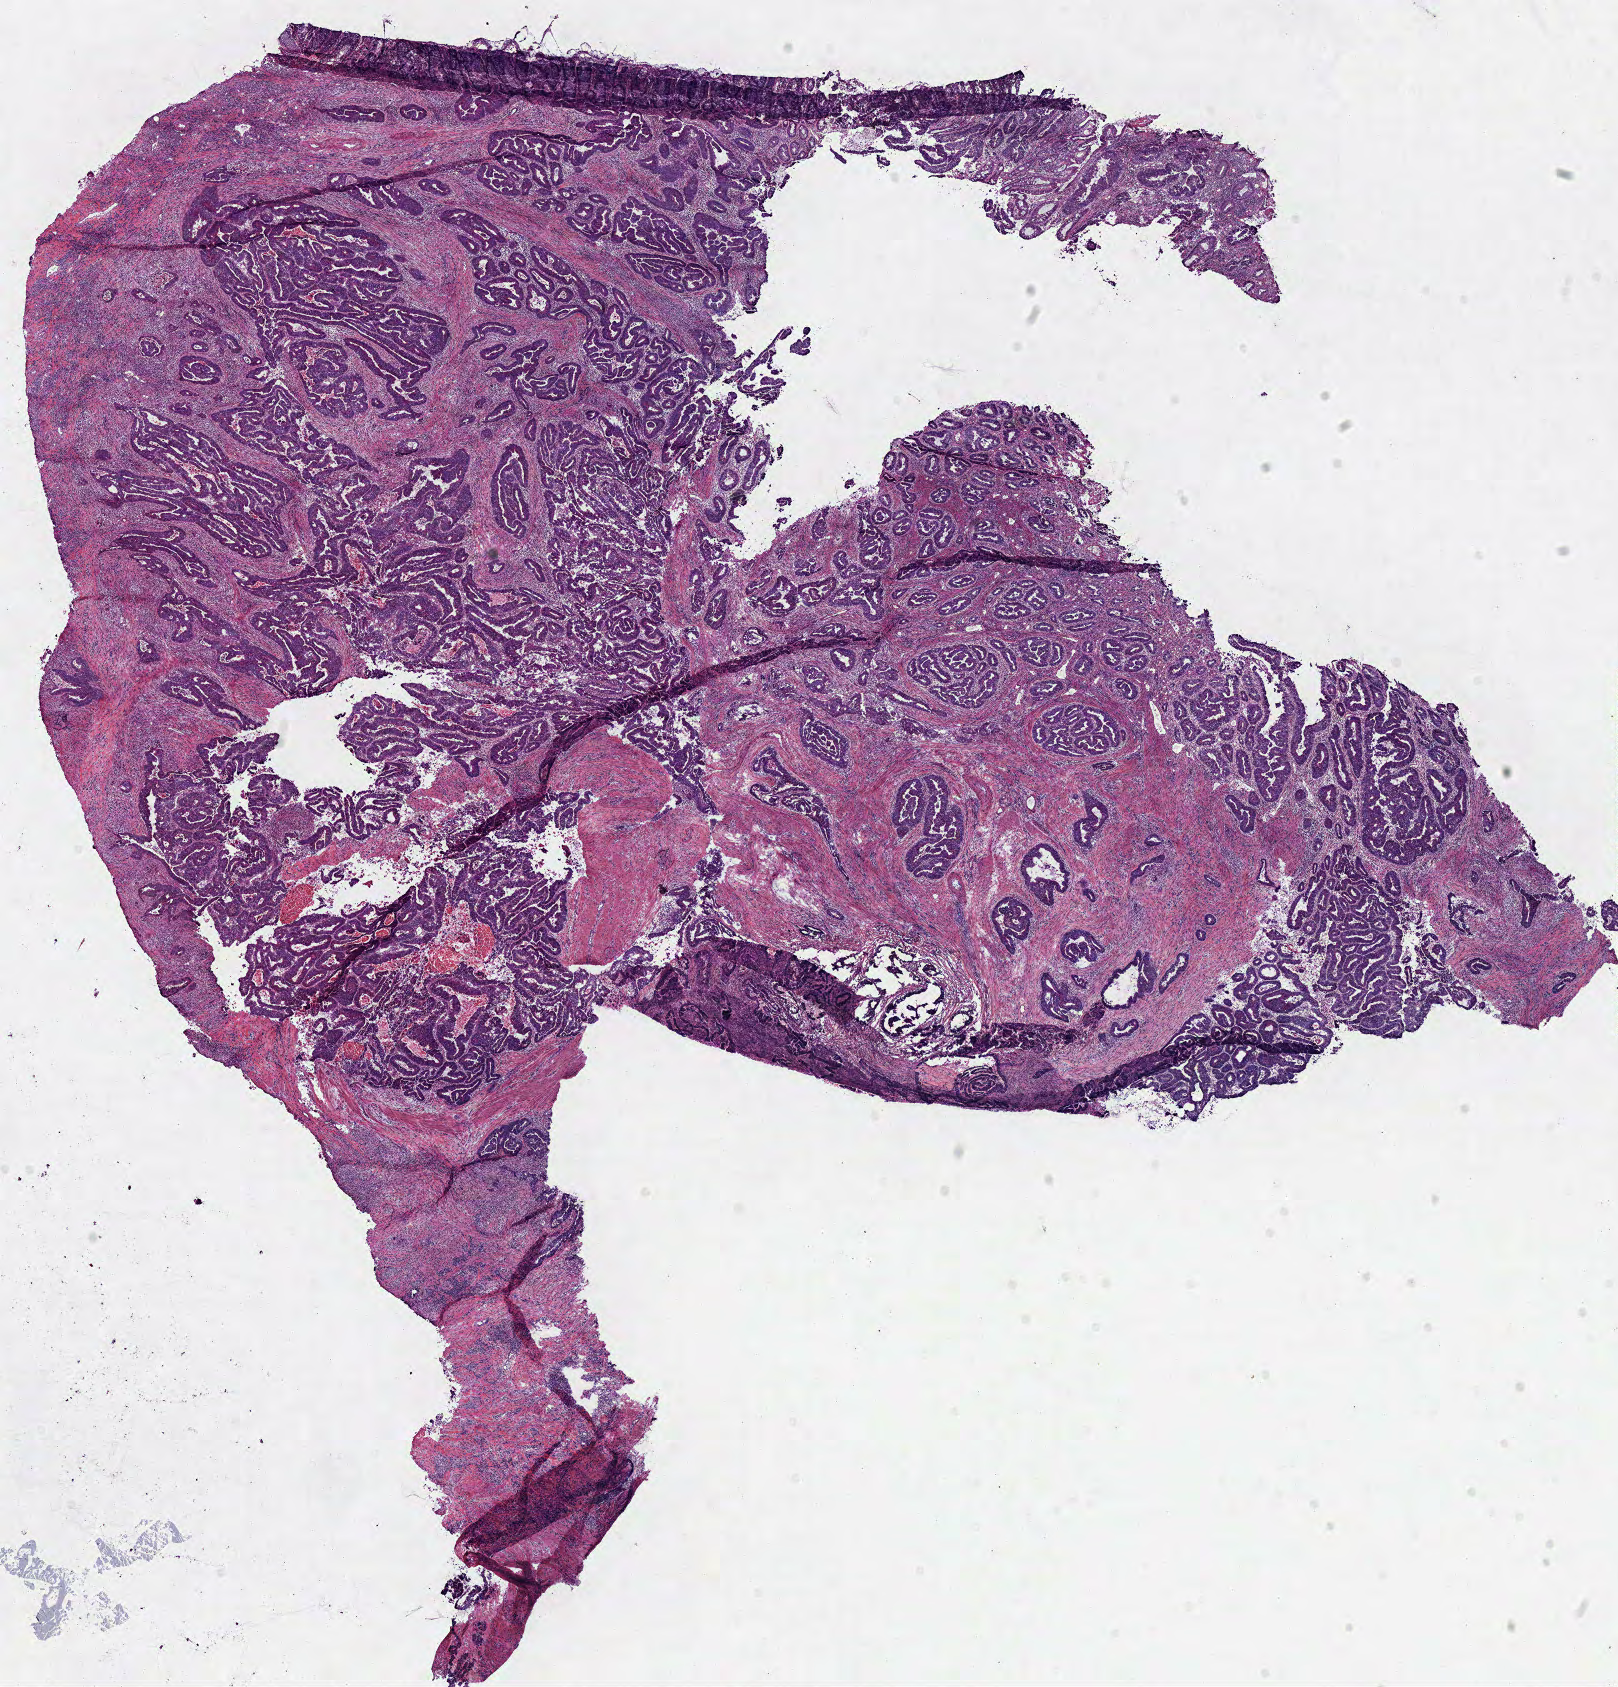
Whole-slide histology image, Hematoxylin and eosin (H&E) stained — whole scanned area (about 12.7 x 13.3 mm) shown as a low-resolution overview; frozen section; sample: primary tumour, colon. Patient: male, age at initial diagnosis 58 years. Slide review estimates, as recorded: tumour cells 70%, tumour nuclei 75%, normal cells 0%, stromal cells 20%, necrosis 10%.
Lymph nodes positive (case pathology): 0 of 21 examined. Diagnosis: Adenocarcinoma, NOS (sigmoid colon). AJCC pathologic stage: IIA (7th edition).